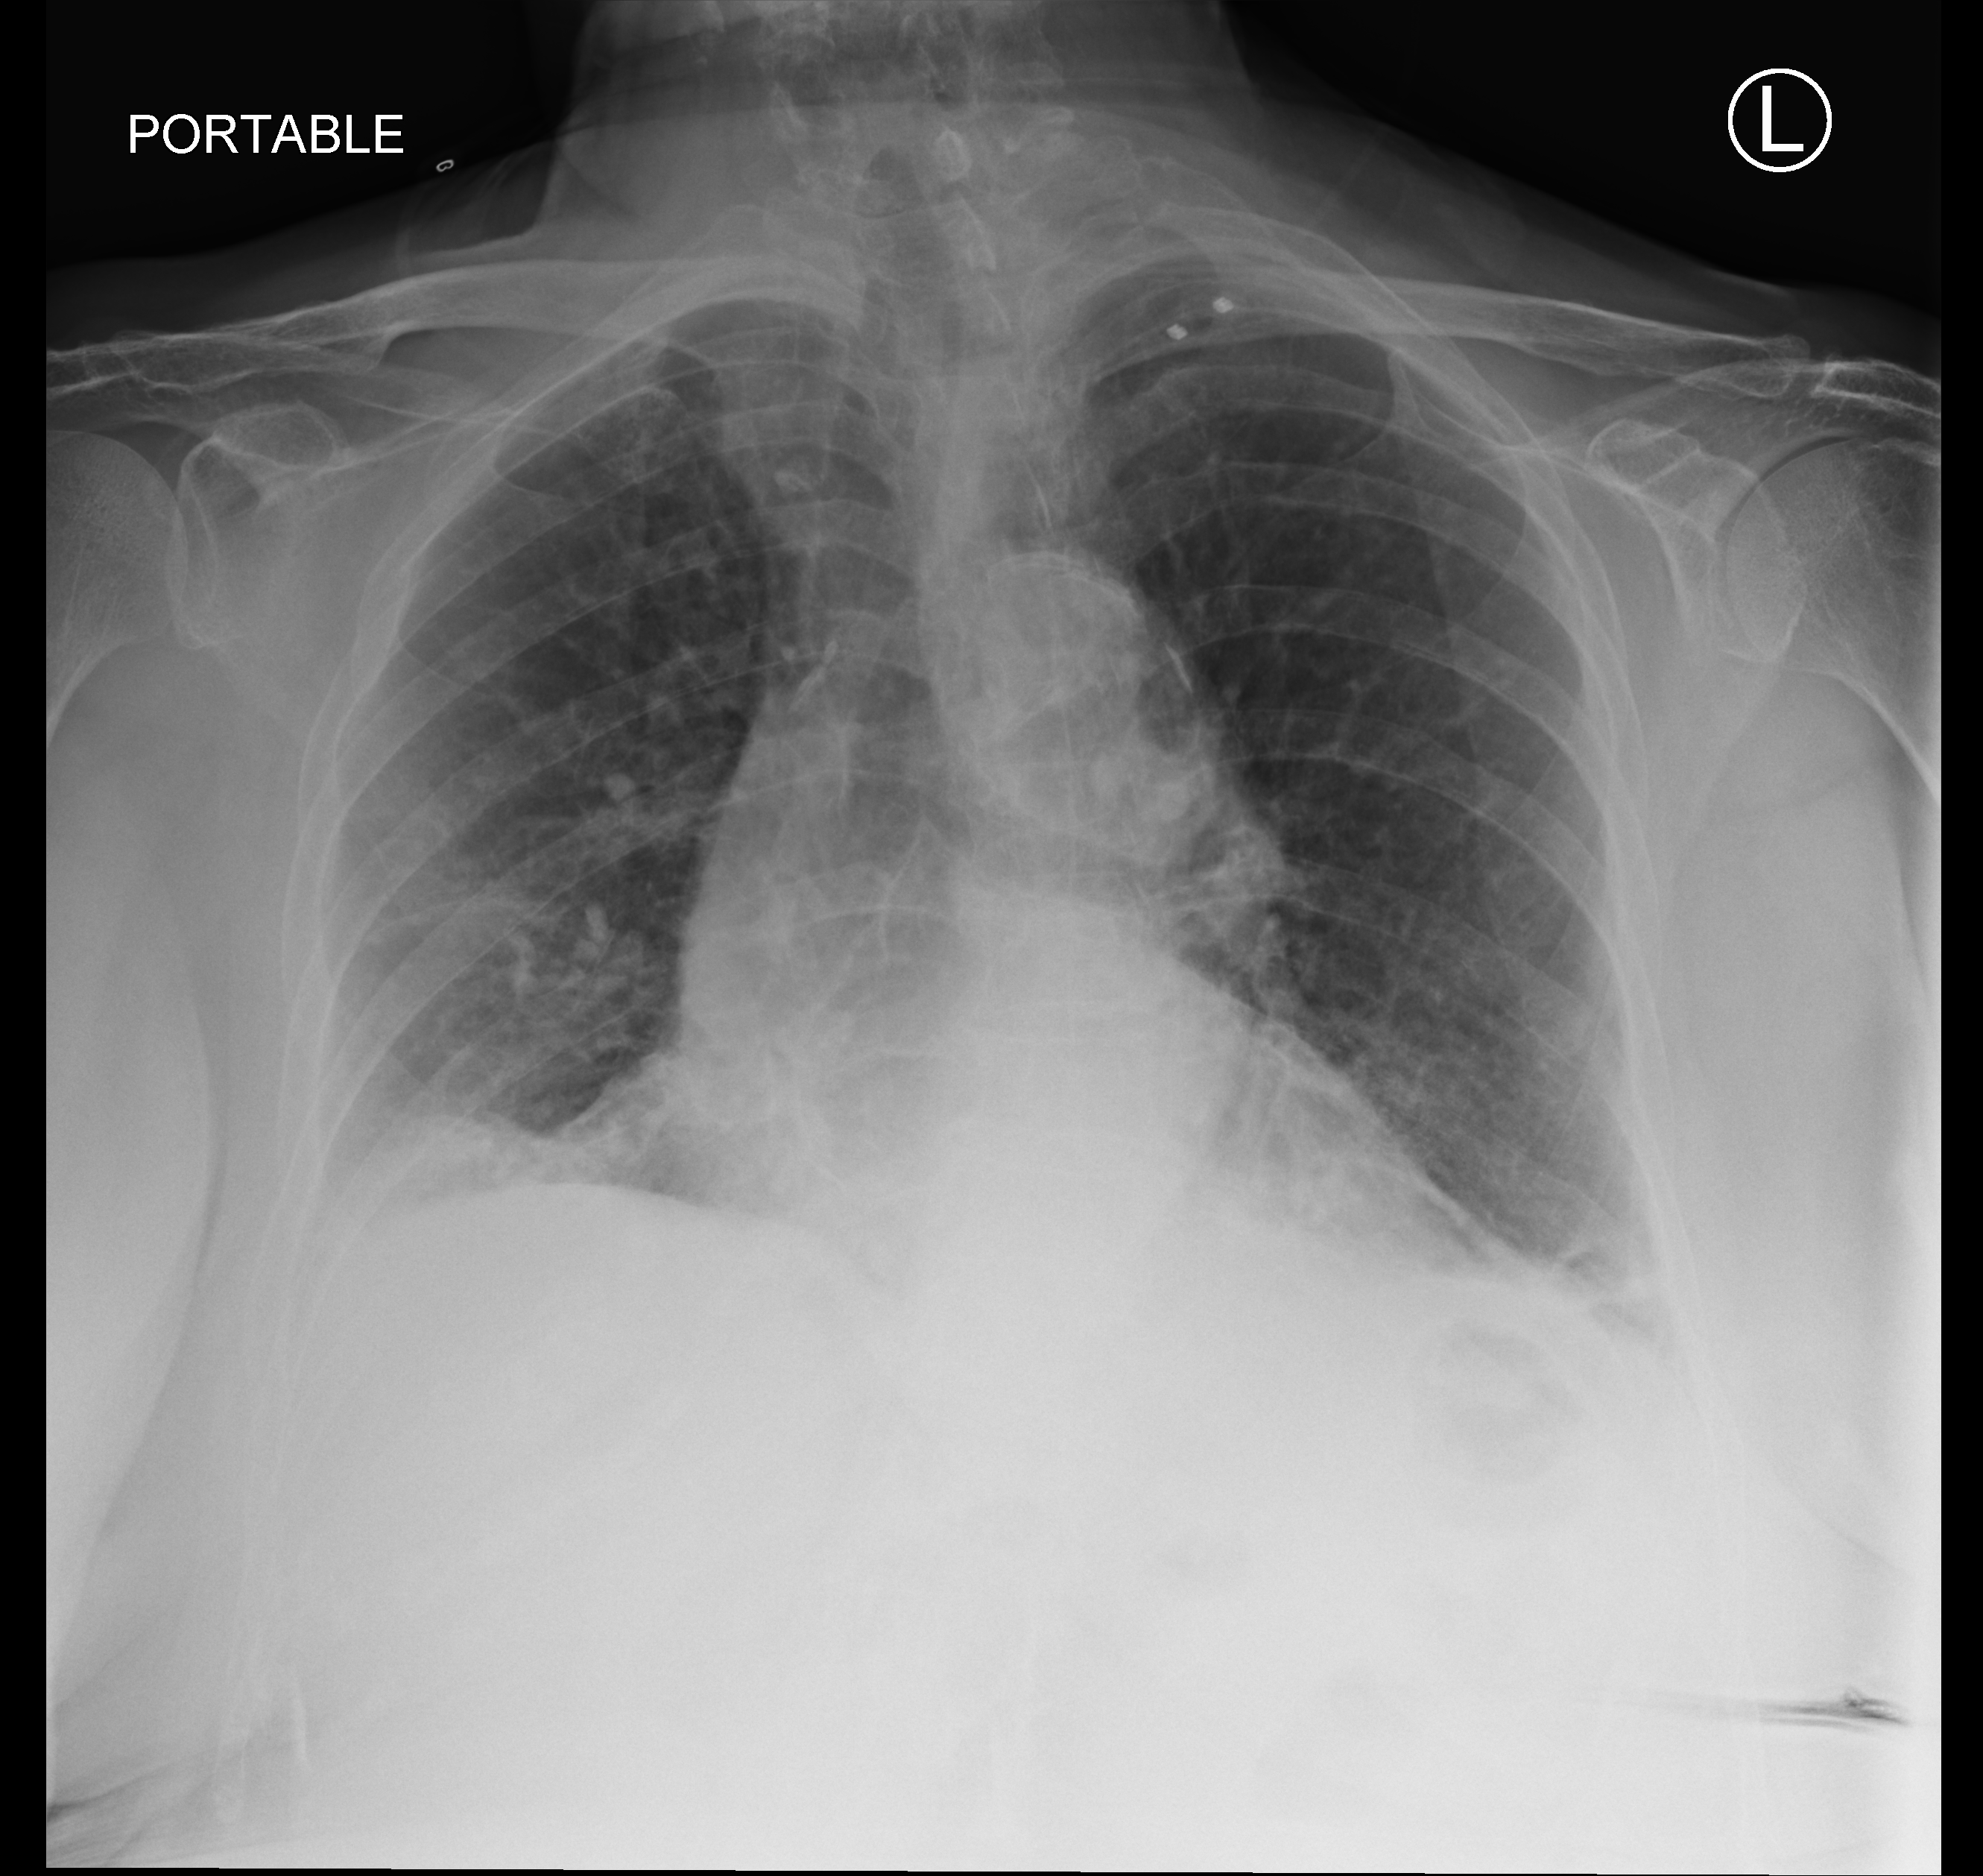
Portable chest radiograph, anteroposterior (AP) projection. Female patient hospitalised with COVID-19, age 75–90 years.
Admission-level facts for this patient (not findings on this image; timing relative to this image not recorded): length of hospital stay: 13 days.